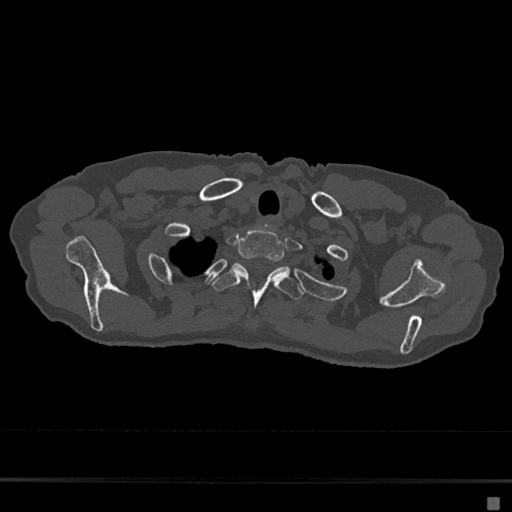
CT including the spine, one axial slice. Position 591 of 797 along the scan axis. Reconstruction kernel Br40s/3. Bone window (W 1800 / L 400 HU). 0.5 mm slice thickness. 512 × 512 image matrix, field of view 360 × 360 mm. Patient: female, 68 years. Case-level facts recorded for this patient, not image findings: primary cancer: renal.
Outlined on this slice (semi-automatically segmented with operator editing):
- T1 vertebra: bounding box <237,228,285,262> (left, top, right, bottom; pixels)
- T2 vertebra: <212,263,304,309>